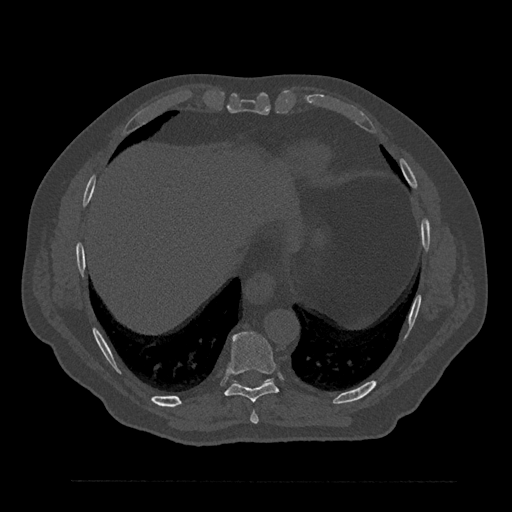
CT including the spine, one axial slice; 120 kVp; bone window (W 1800 / L 400 HU); 512 × 512 image matrix, field of view 430 × 430 mm. Male patient, age 61 years. From the clinical record (not read from this slice): primary cancer: prostate.
Annotated regions visible in this slice (semi-automatic segmentation, software-assisted and operator-edited):
- T8 vertebra: bounding box (x1, y1, x2, y2) in pixels: (250, 411, 259, 424)
- T9 vertebra: (224, 332, 279, 403)